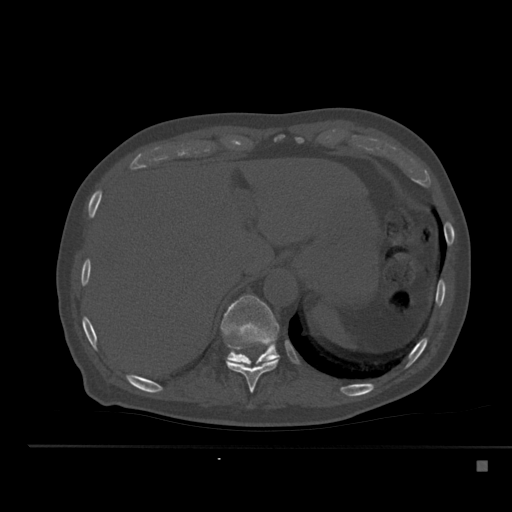
CT including the spine, one axial slice; slice 261 of 517 in the series (ordered by position); reconstruction kernel Br40s; 120 kVp; bone window (W 1800 / L 400 HU); 1.5 mm slice thickness; 512 × 512 image matrix, field of view 408 × 408 mm. Patient: male, 70 years. Case-level facts recorded for this patient, not image findings: primary cancer: renal.
Outlined on this slice (semi-automatically segmented with operator editing):
- T10 vertebra: bounding box [x1, y1, x2, y2] px = [226, 347, 279, 393]
- T11 vertebra: [220, 295, 280, 364]